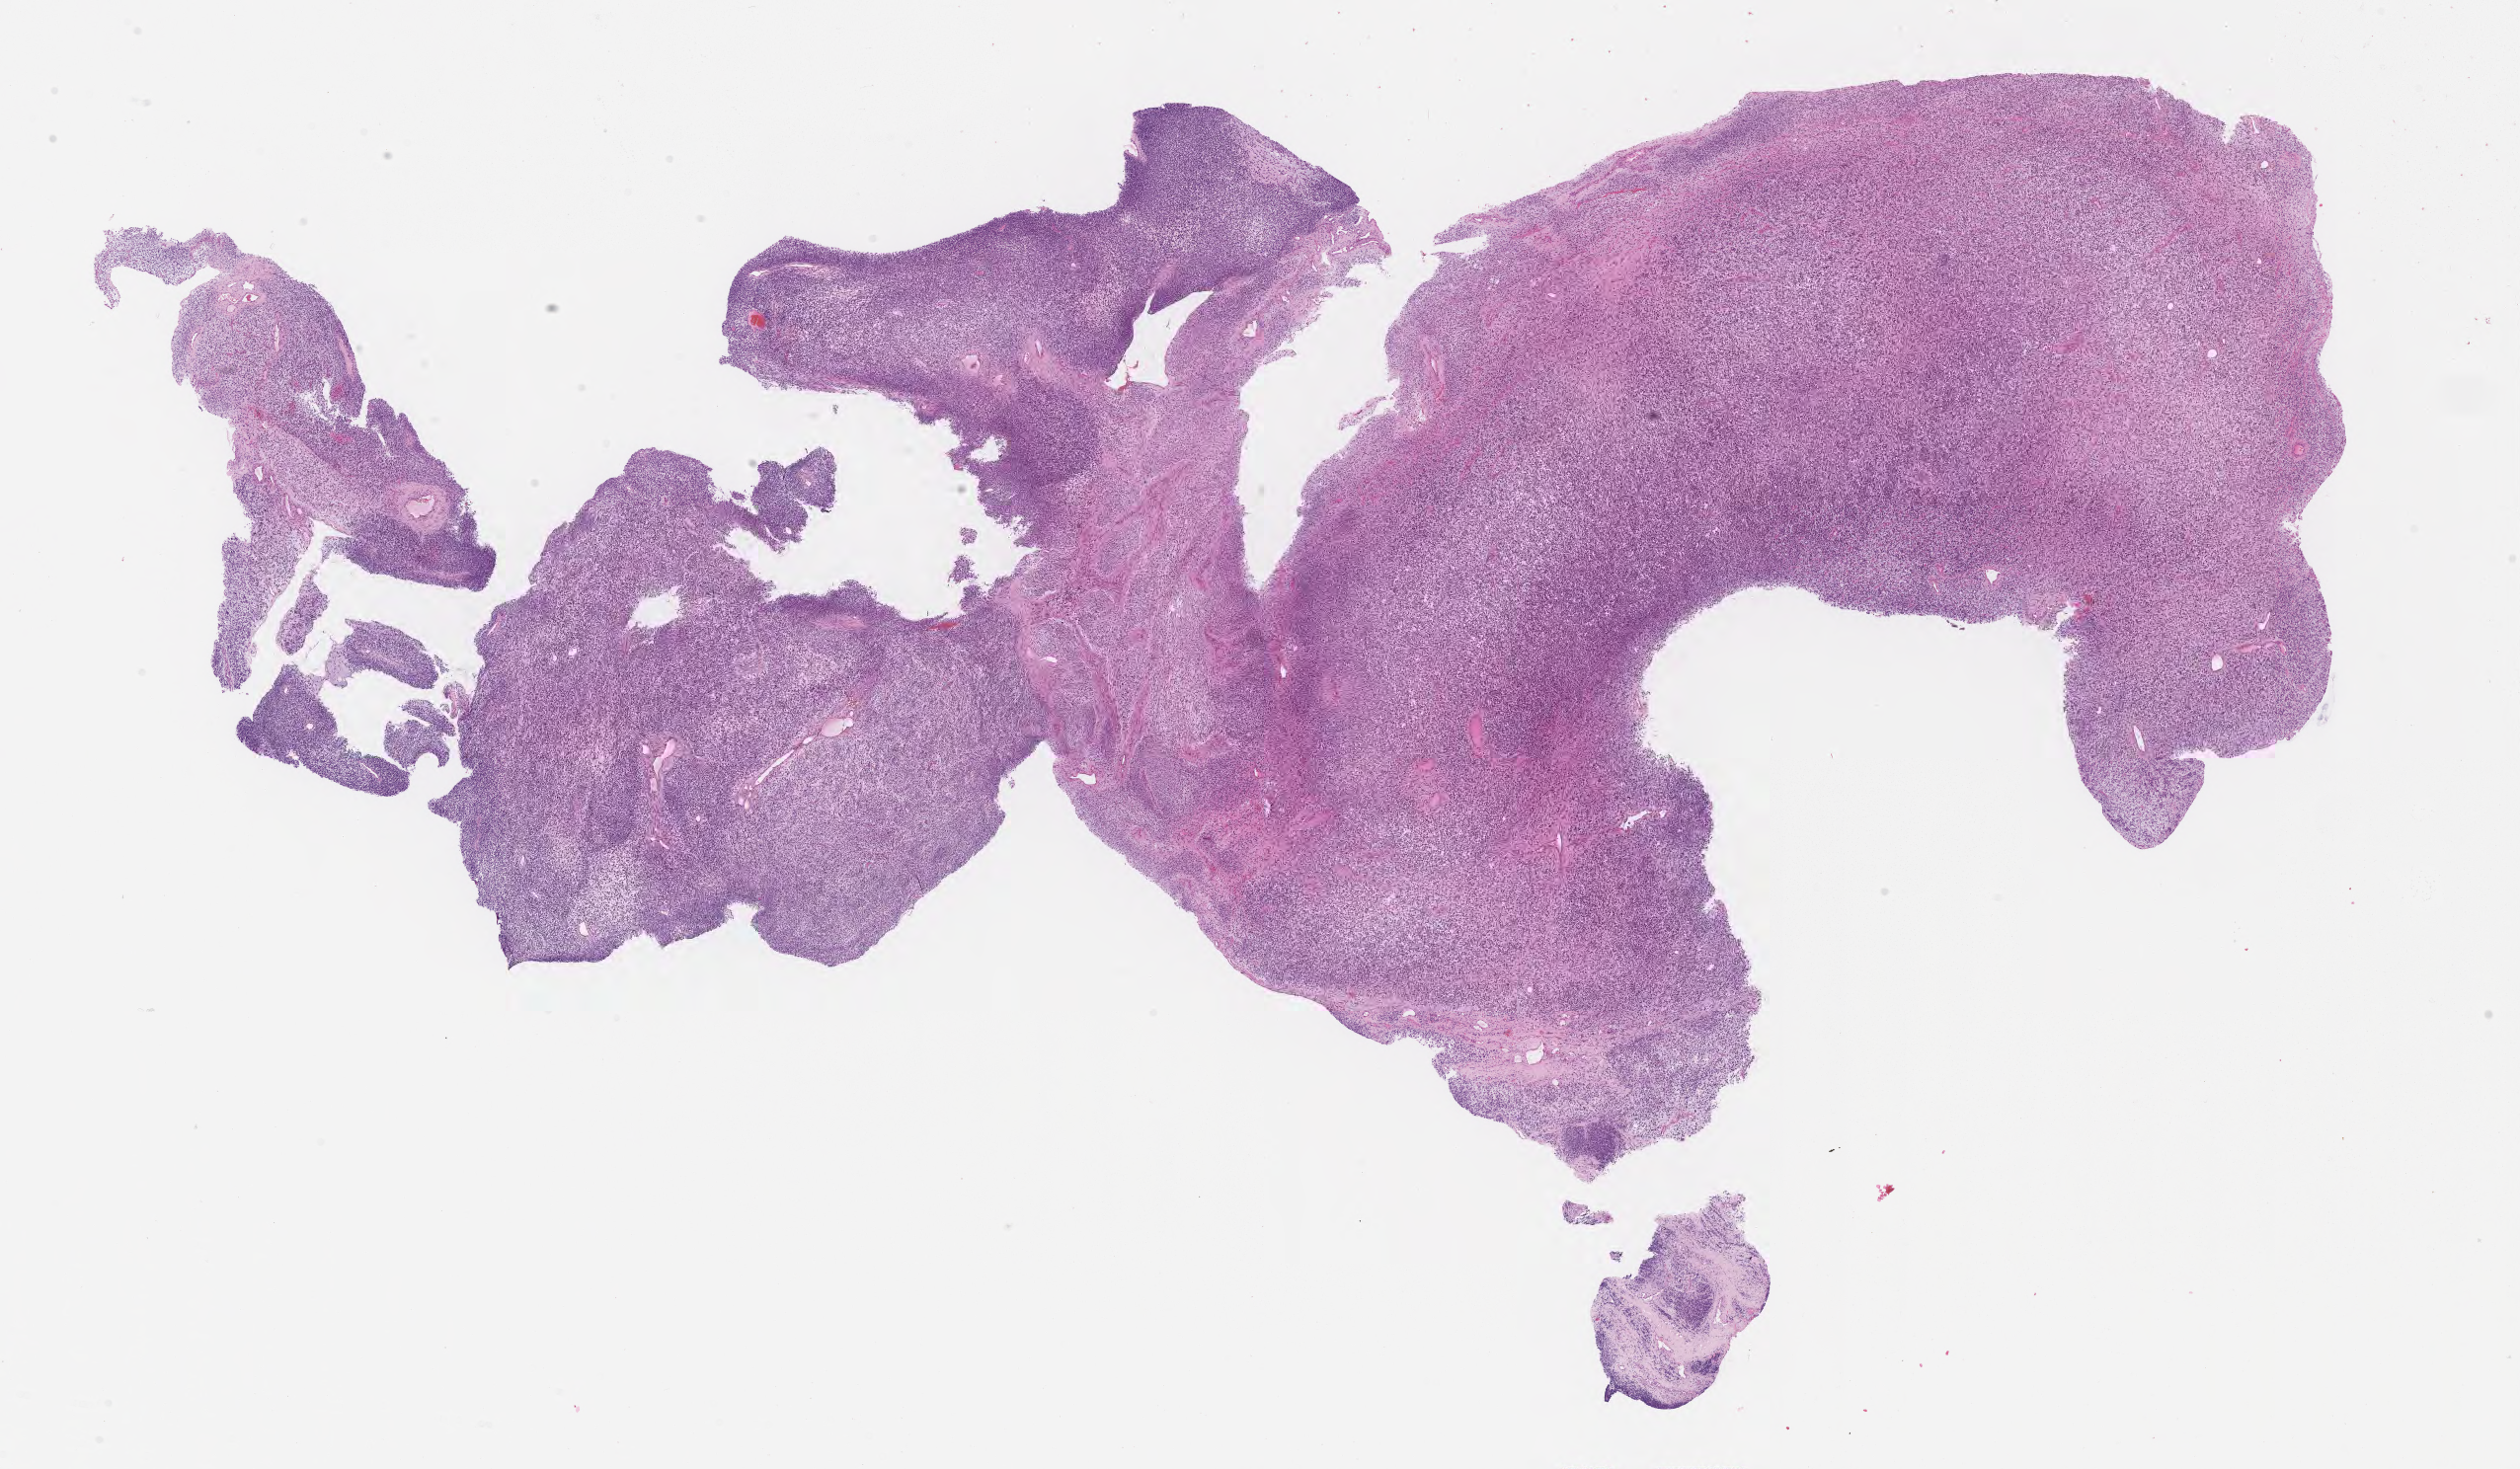
Whole-slide image, H&E stain of tumor tissue — a low-resolution overview of the entire scanned area, about 20.6 x 12.0 mm, FFPE section, site: soft tissue, pelvis-left. Patient: male, age 4.3 years at diagnosis.
* stage (as recorded): 3
* diagnosis: rhabdomyosarcoma; histological classification: embryonal rhabdomyosarcoma
* metastatic status at presentation (as recorded): non-metastatic (unconfirmed)